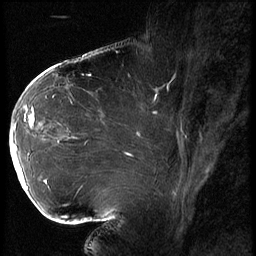
Breast MRI (dynamic contrast-enhanced), one sagittal slice; slice 38 of 62 in the series (ordered by position); 3 images stored at this slice position (order not interpretable as contrast timing); 1.5 T; TE 4.2 ms, TR 9 ms; 256 × 256 image matrix, field of view 180 × 180 mm. Female patient, age 43 years. Case-level facts recorded for this patient, not image findings: setting: breast cancer imaged before/during neoadjuvant chemotherapy; receptor status: HER2-positive.
Annotated regions visible in this slice (semi-automatic segmentation, software-assisted and operator-edited):
- analysis volume of interest (the breast-tissue region the enhancement analysis was run in; not a lesion): bounding box (x1, y1, x2, y2) in pixels: (11, 90, 82, 203)
- tumour enhancement mask (voxels above the 140 % enhancement threshold inside the analysis volume of interest): (11, 107, 47, 189)